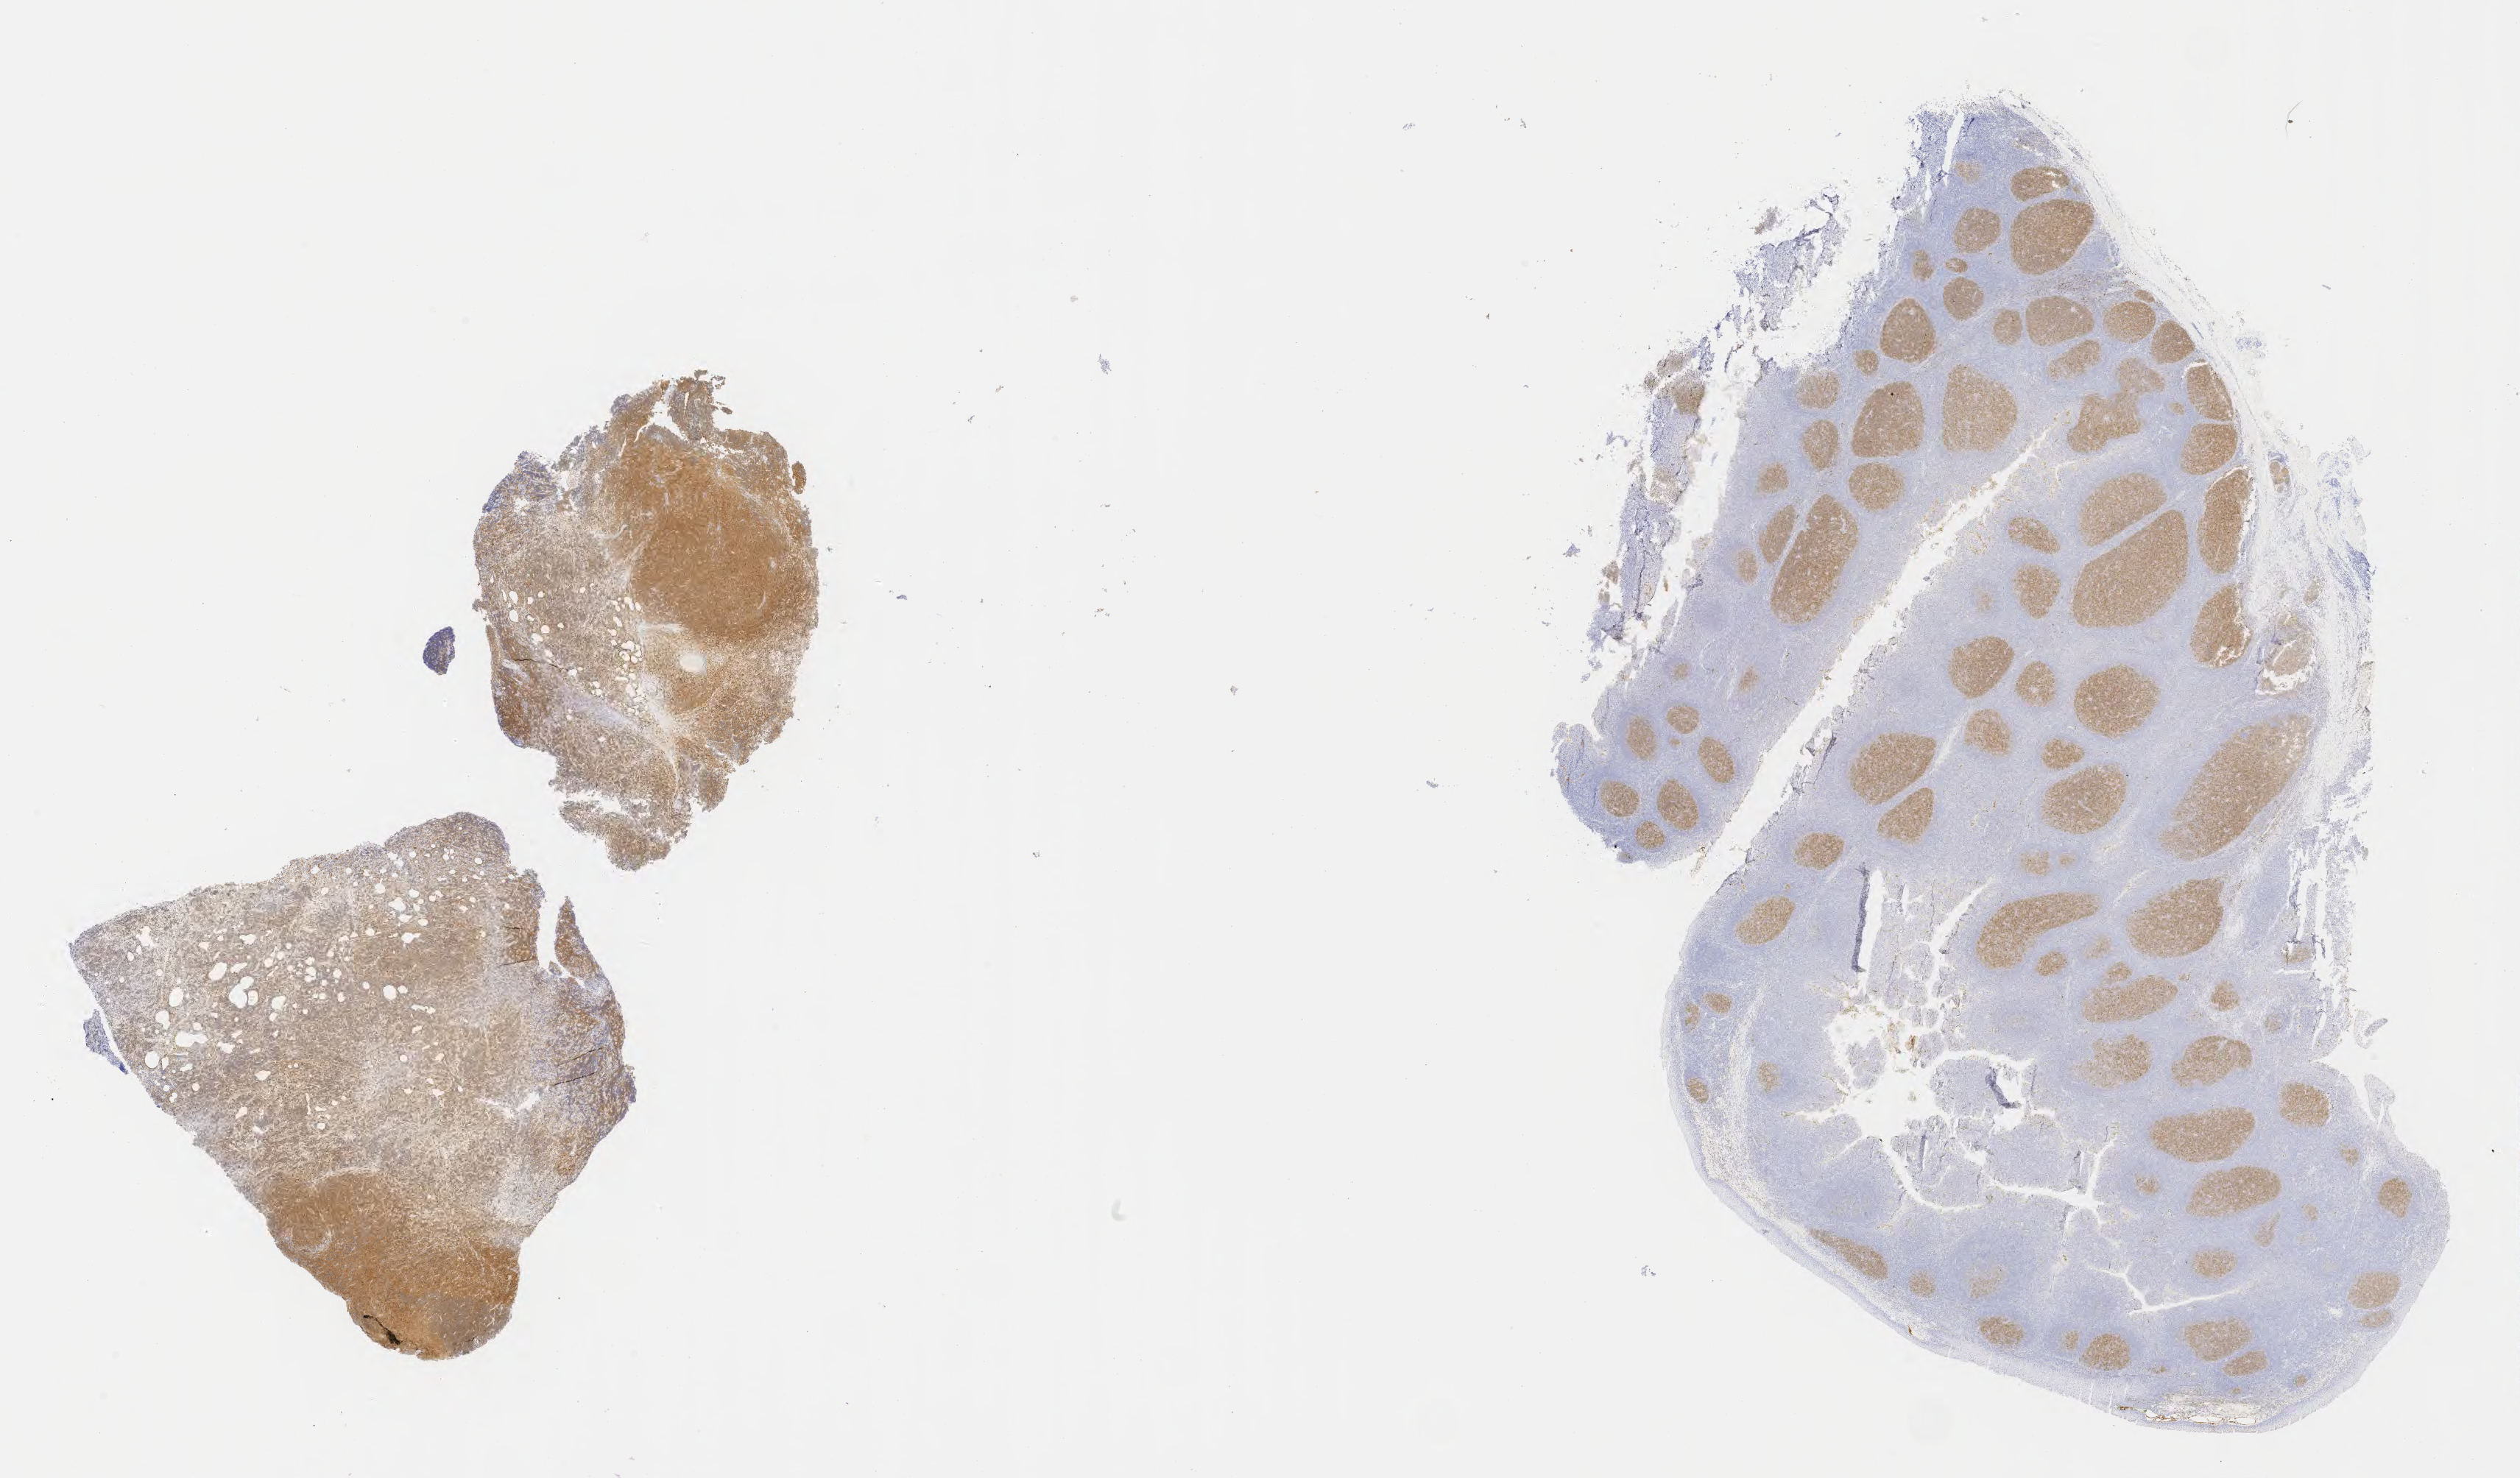
Immunohistochemistry (IHC) whole-slide image stained for CD10, a low-resolution overview of the entire scanned area, about 27.7 x 16.2 mm. Specimen: tumor tissue. Anatomic site: mandible. Patient: male, age at initial diagnosis 7 years.
• histologic diagnosis: Burkitt lymphoma, NOS